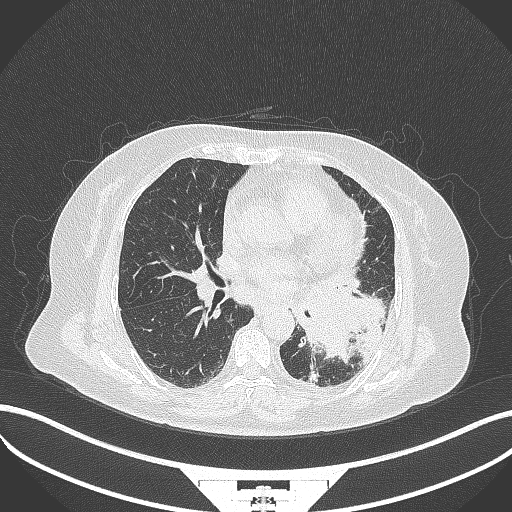
Chest CT, one axial slice. Position 173 of 322 along the scan axis. Lung window (W 1500 / L -600 HU). 1 mm slice thickness. 512 × 512 image matrix, field of view 400 × 400 mm. Female patient, age 69 years. From the clinical record (not read from this slice): clinical TNM (as recorded): T2b N3 M1.
Structures marked on this image (rectangle marked by the reading radiologist):
- lung tumour (recorded histology: adenocarcinoma): bounding box [x1, y1, x2, y2] px = [298, 268, 387, 363]